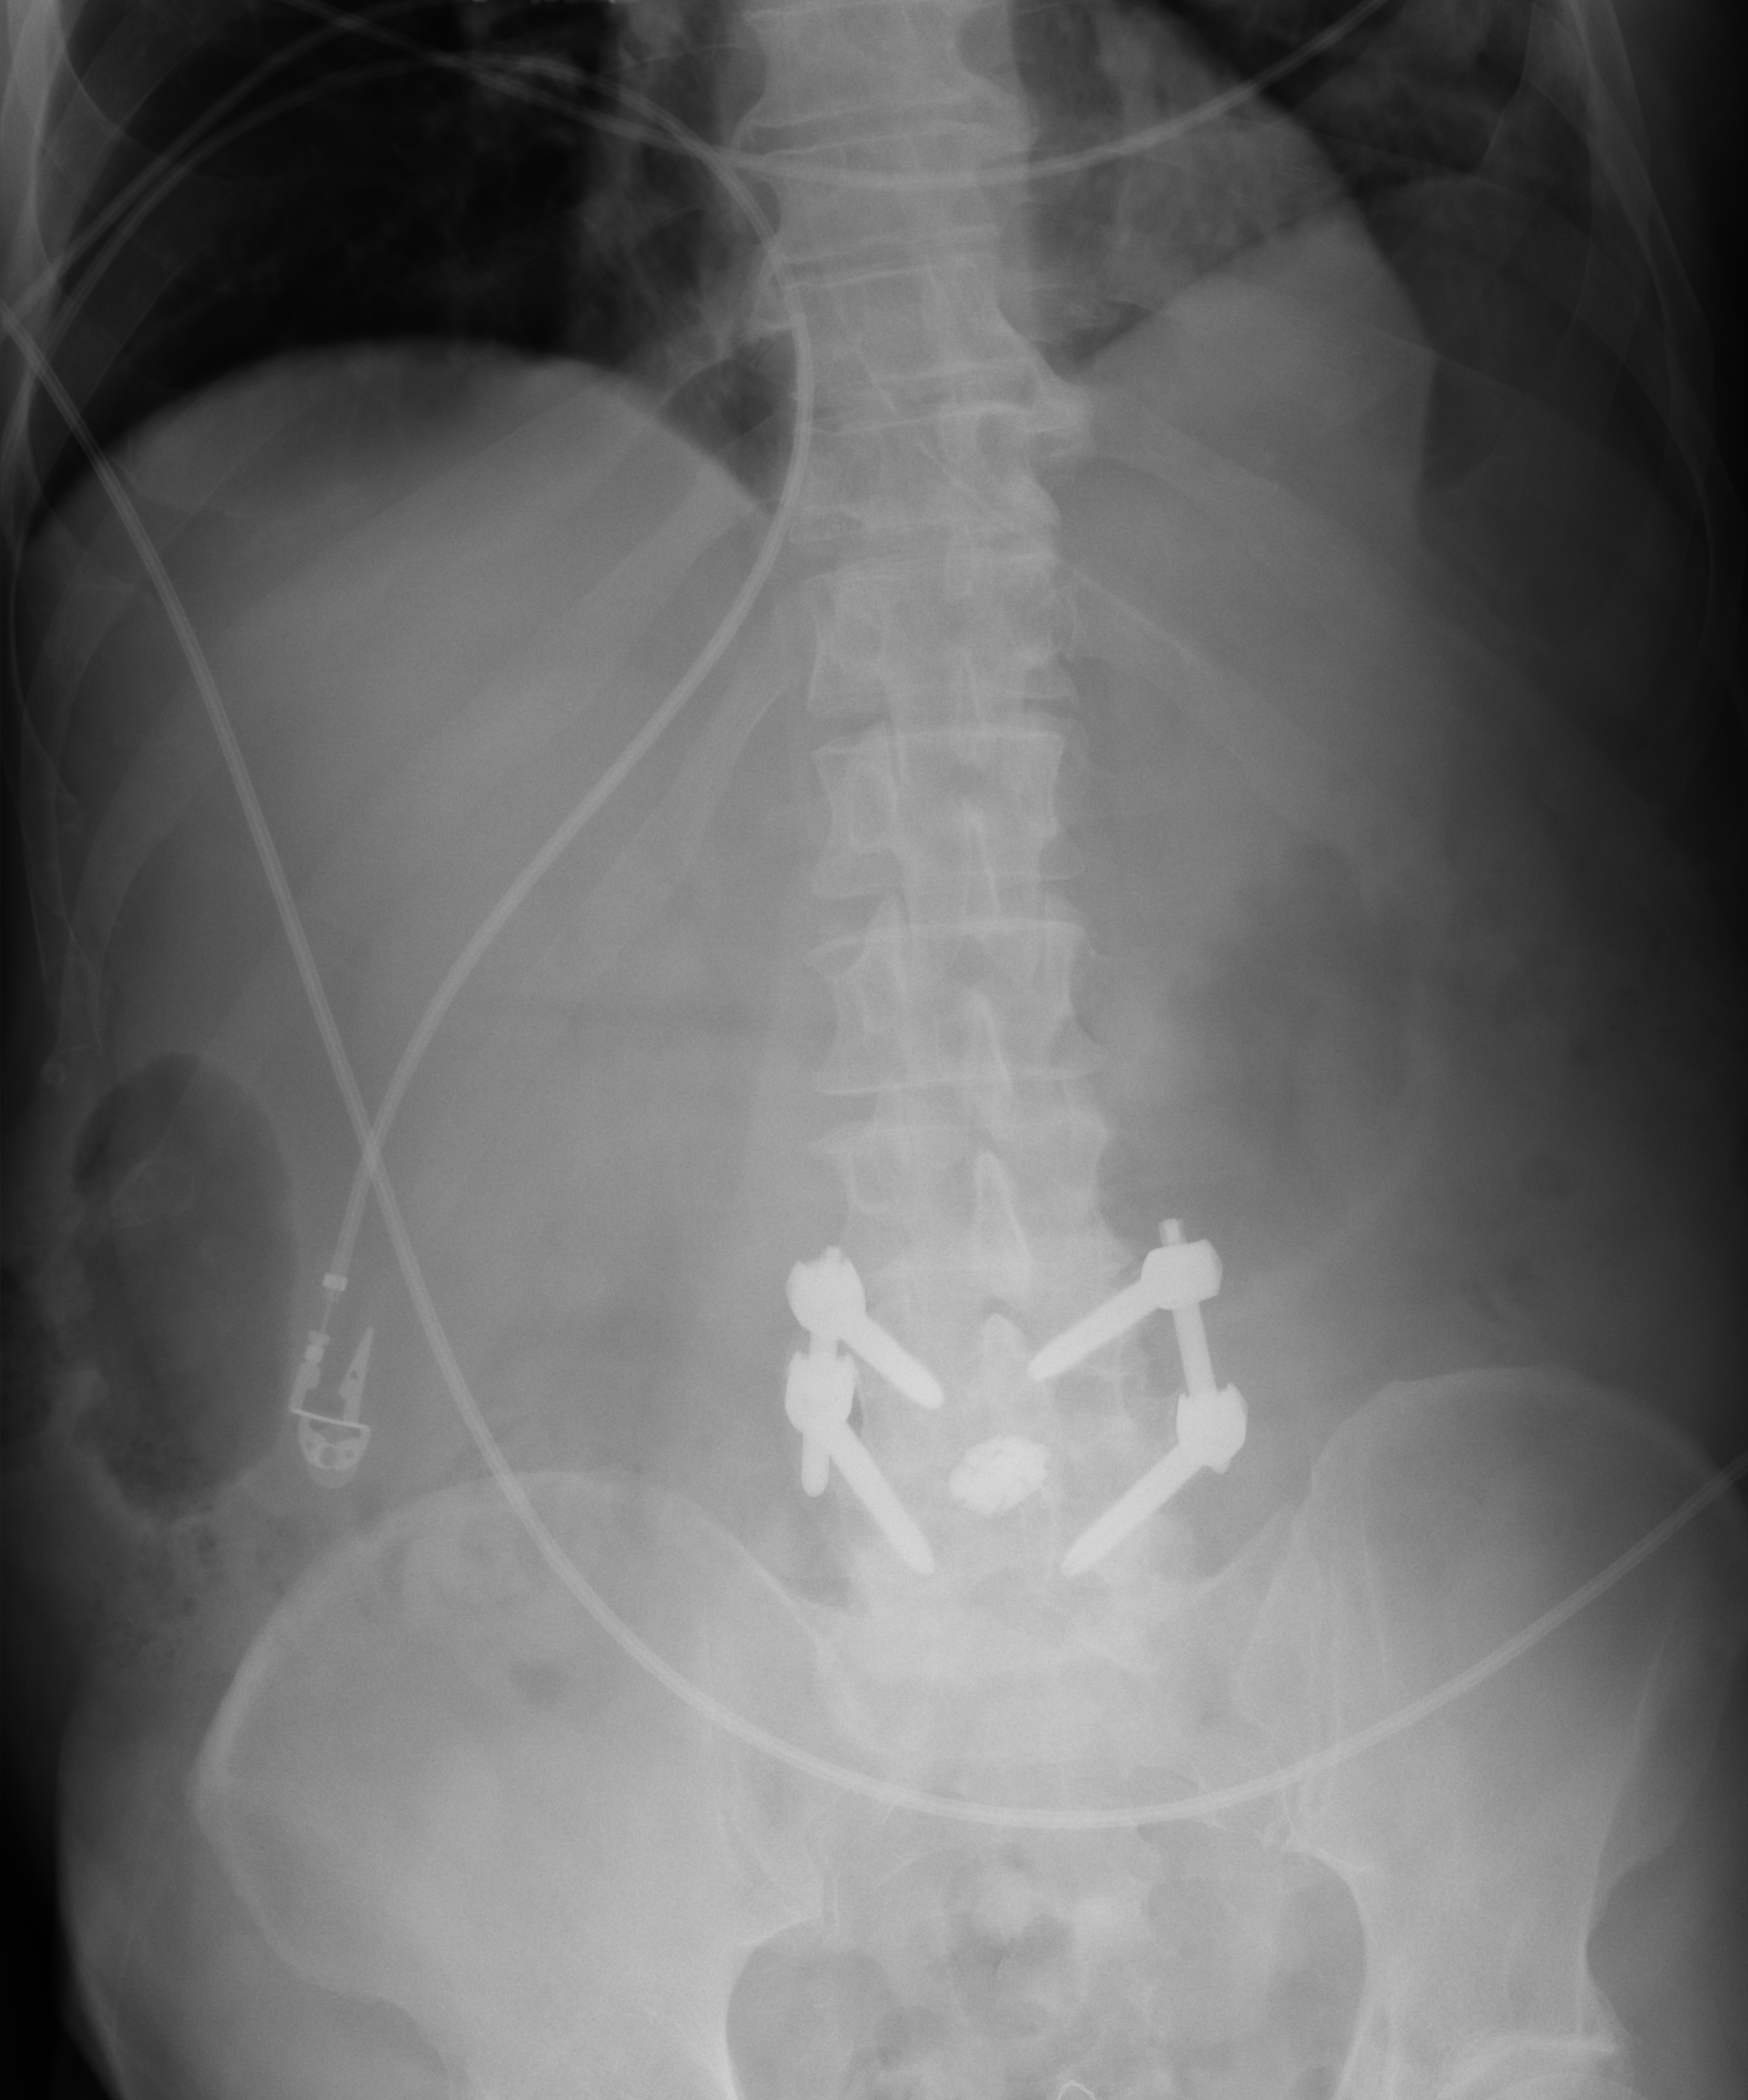
Abdomen X-ray (portable), anteroposterior (AP) projection. Patient hospitalised with COVID-19; male, aged 60–74 years.
From the hospital-stay record, not from the radiograph (when in the stay this image was taken is not recorded):
- length of hospital stay: 35 days
- mechanically ventilated during this hospital stay: yes